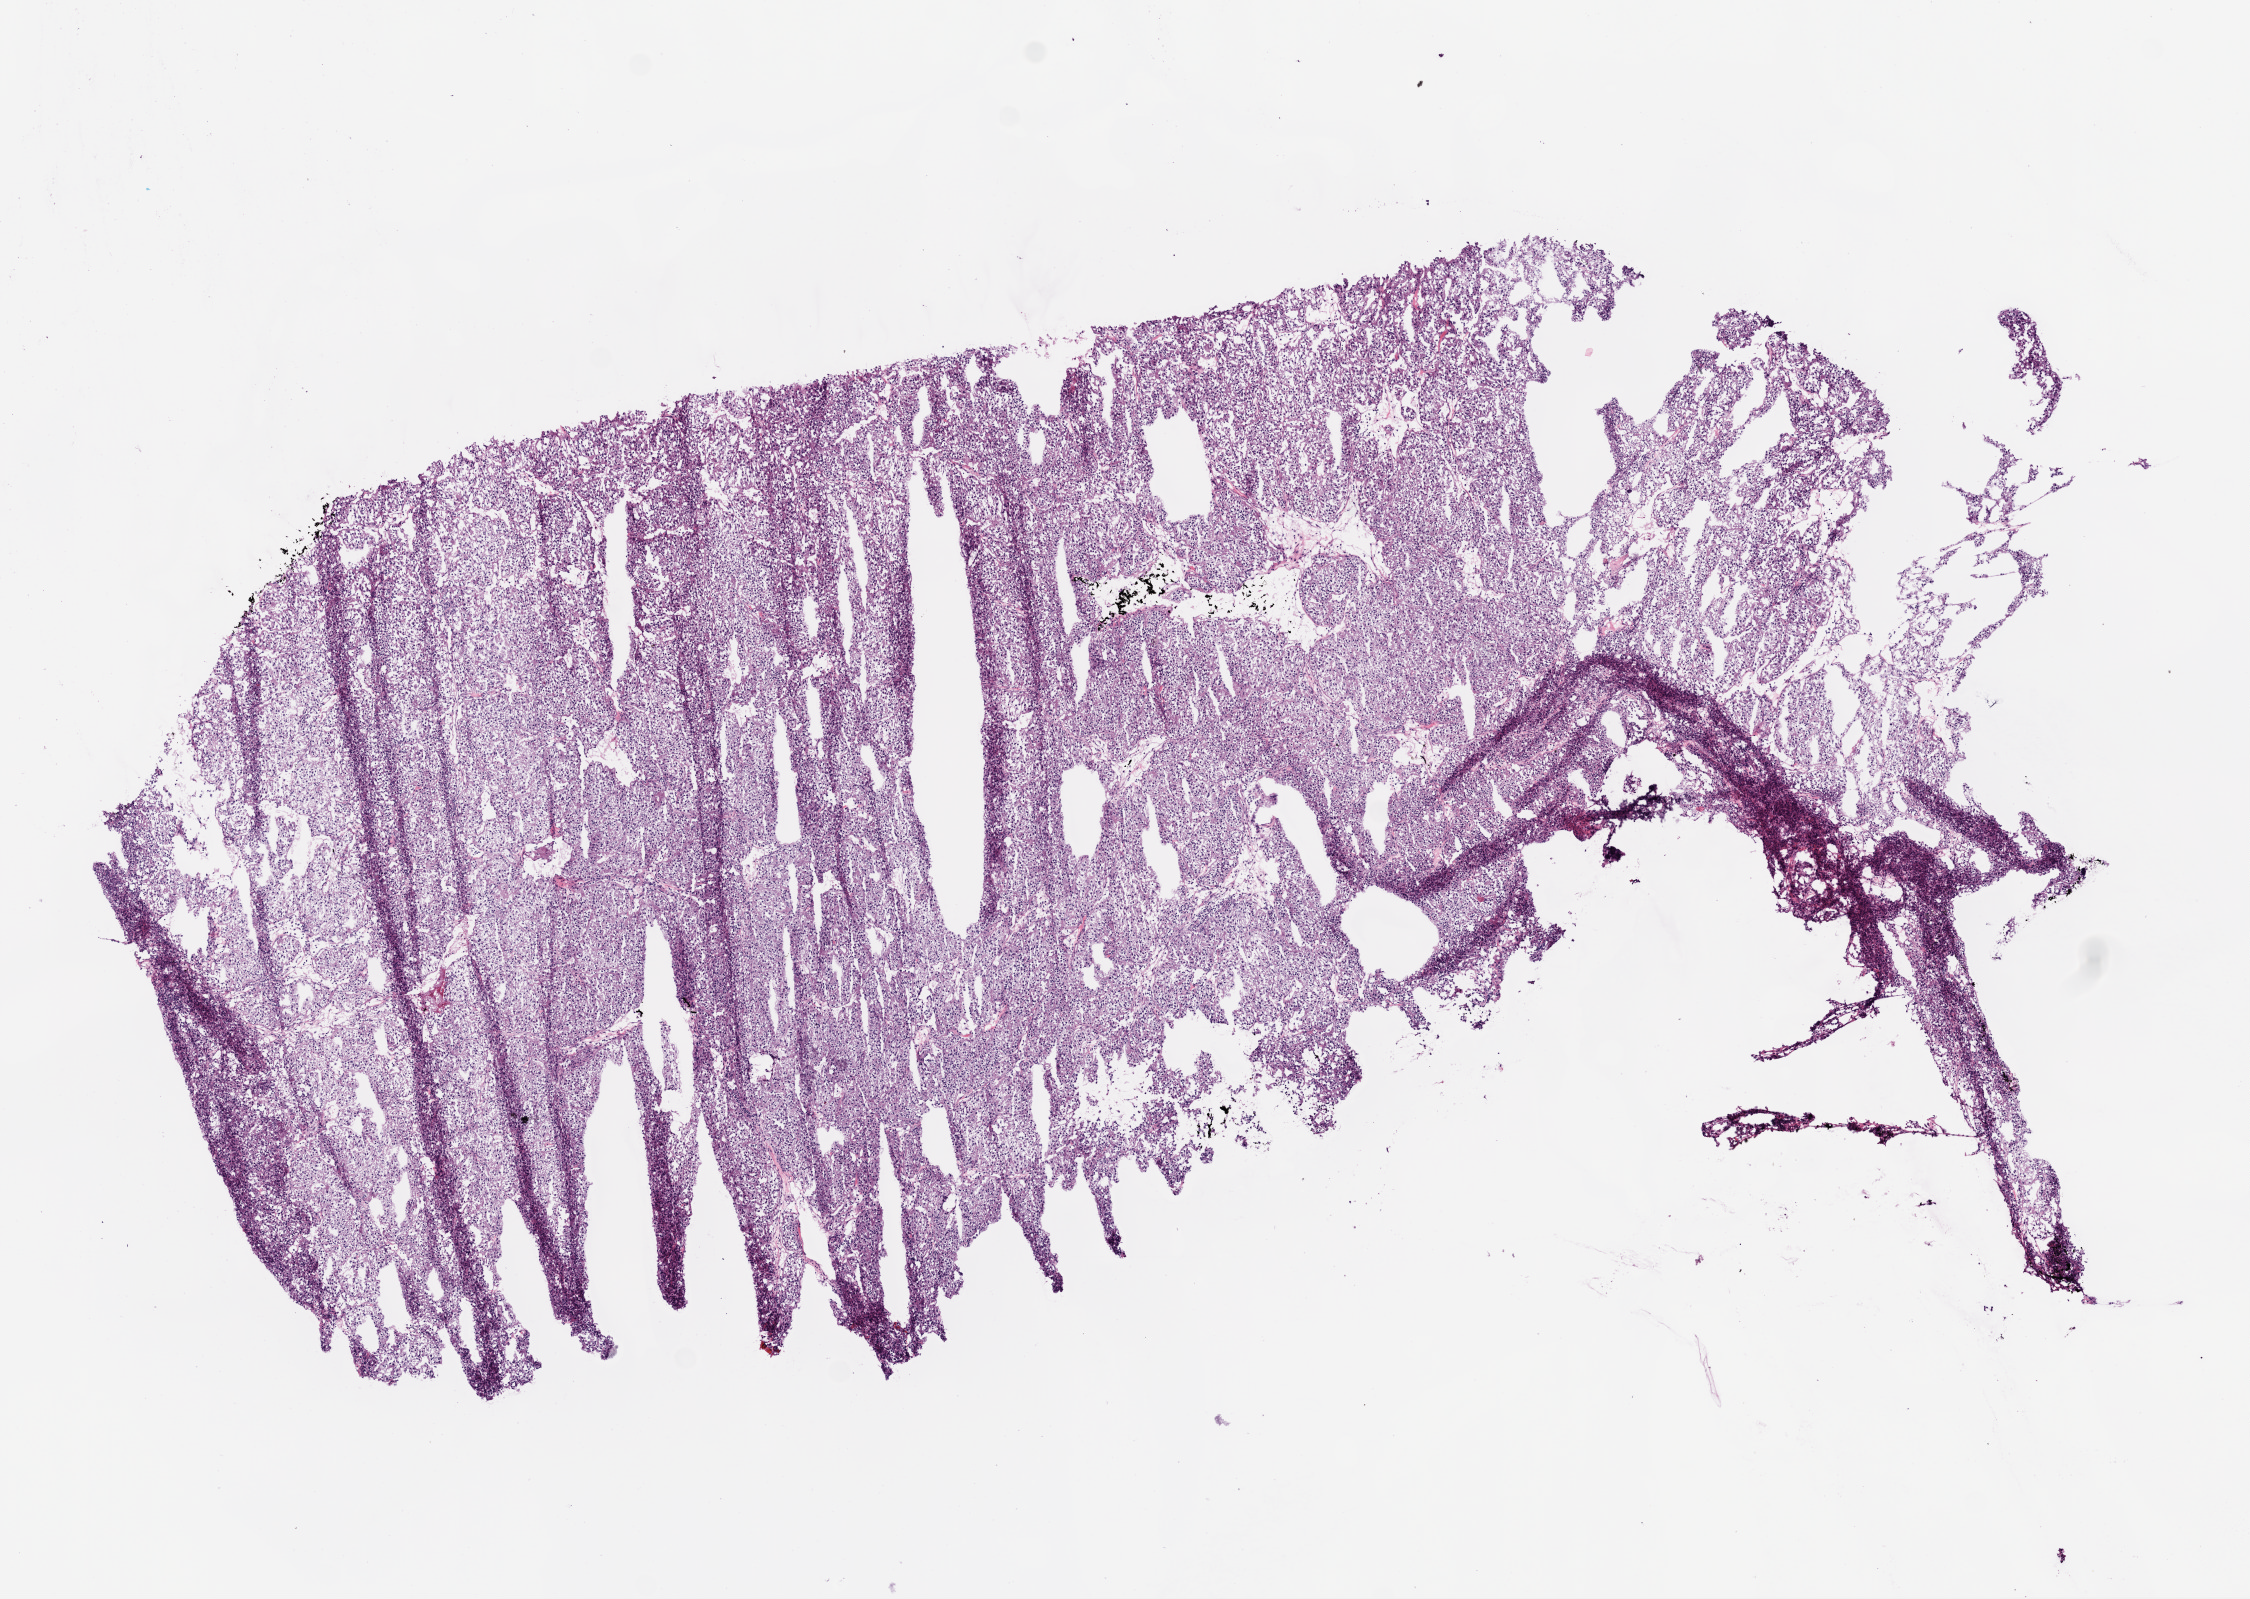
Digitized Hematoxylin and eosin (H&E) stained tissue section (whole slide) — shown as a low-resolution overview of the whole scanned area (about 9.0 x 6.4 mm); frozen section from the bottom of the tissue portion; sample: primary tumour, kidney. Male, age 67 years at initial diagnosis. Histologic grade: G3 (poorly differentiated). Pathologist review of this section (percent, as recorded): tumour cells 95%, tumour nuclei 90%, normal cells 0%, stromal cells 5%, necrosis 0%.
TNM: T1b N0 M0. AJCC pathologic stage: I. Laterality: left. Diagnosis: Clear cell adenocarcinoma, NOS.